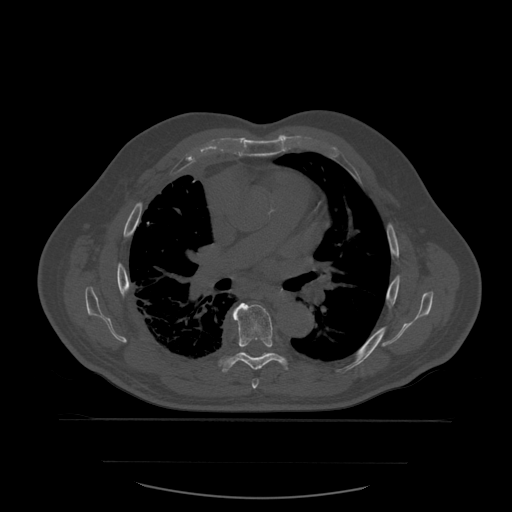
CT including the spine, one axial slice; position 384 of 590 along the scan axis; bone window (W 1800 / L 400 HU); 512 × 512 image matrix. Patient age 71 years. Case-level facts recorded for this patient, not image findings: primary cancer: lung; vertebrae with lytic lesions (as recorded): T1, T2, L5, S1.
Outlined on this slice (semi-automatically segmented with operator editing):
- T6 vertebra: box from (x=252, y=379) to (x=259, y=389) px
- T7 vertebra: (x=218, y=303)–(x=289, y=373)